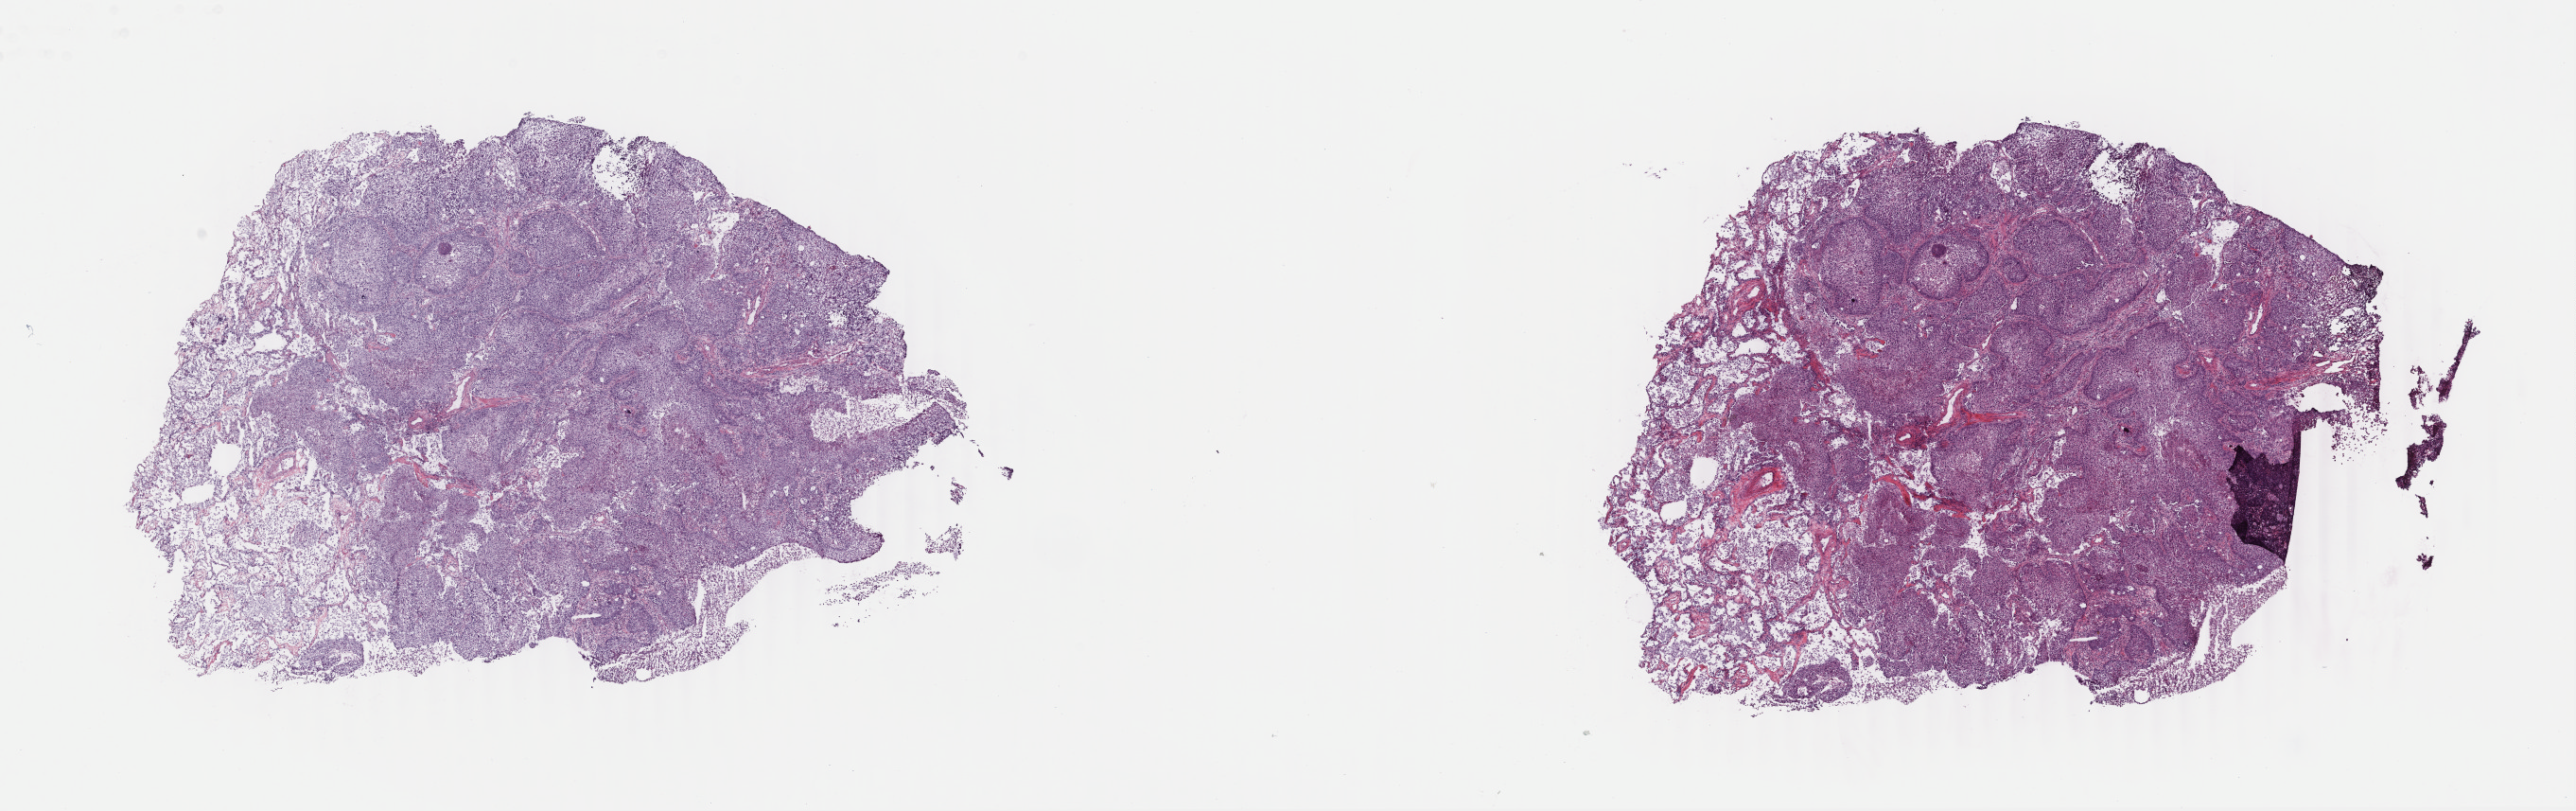
Digitized H&E tissue section (whole slide), shown as a low-resolution overview of the whole scanned area (about 21.7 x 6.8 mm, slide scanned at 40x); frozen section from the top of the tissue portion; sample: primary tumour, lung. Patient: male, age at initial diagnosis 71 years. Slide review estimates, as recorded: tumour cells 85%, tumour nuclei 85%, normal cells 0%, stromal cells 15%, necrosis 0%. Infiltration values recorded for this section: lymphocyte infiltration 5%, monocyte infiltration 0%, neutrophil infiltration 0%.
AJCC pathologic stage: IB. Pathologic diagnosis: Squamous cell carcinoma, NOS.